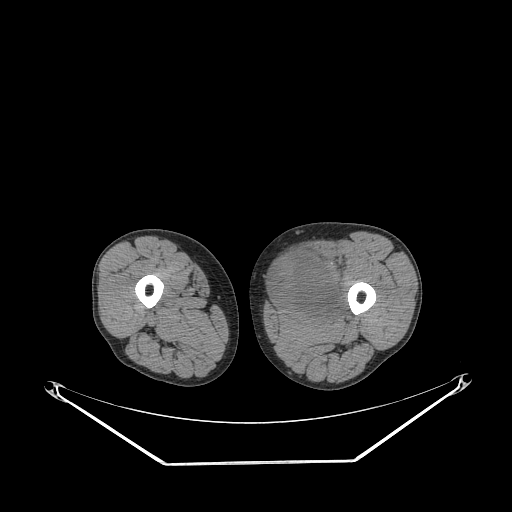
CT of an extremity soft-tissue mass (from a PET/CT study), one axial slice; position 234 of 267 along the scan axis; soft-tissue window (W 400 / L 40 HU); 3.75 mm slice thickness; 512 × 512 image matrix, field of view 500 × 500 mm. Male patient. From the clinical record (not read from this slice): histological type: pleiomorphic liposarcoma; grade: high; site of the primary tumour: left thigh.
Structures marked on this image (expert contour drawn on MRI and transferred to this co-registered scan by the dataset authors):
- gross tumour volume including surrounding oedema: box from (x=272, y=247) to (x=348, y=321) px
- gross tumour volume (mass): (x=272, y=251)–(x=339, y=314)